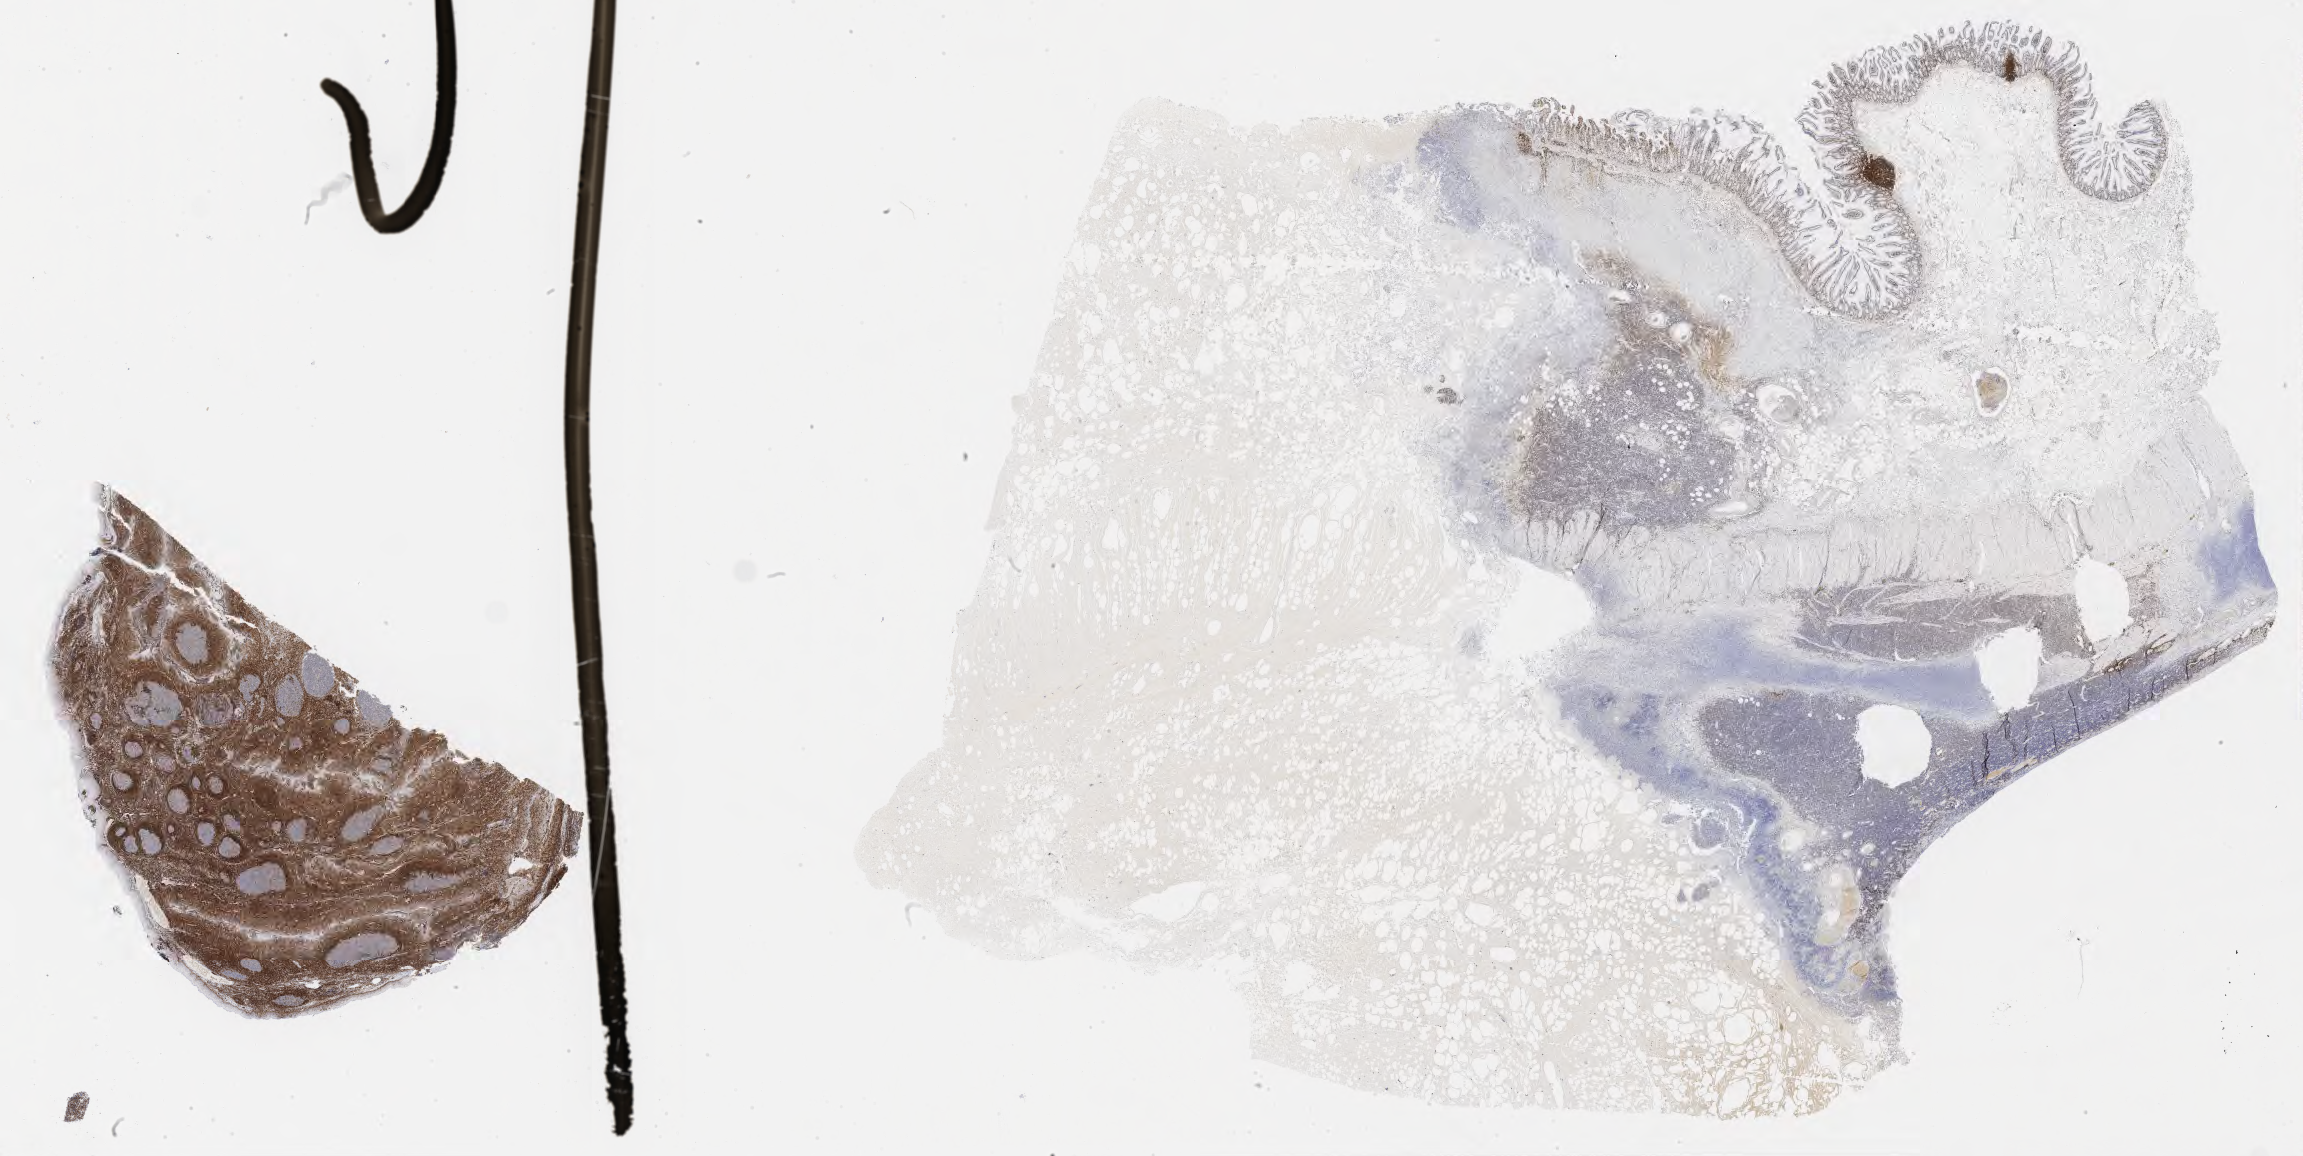
Whole-slide image, immunohistochemical stain for BCL2, a low-resolution overview of the entire scanned area, about 37.2 x 18.7 mm, tumor tissue, site: colon. Patient male; 62 years old.
Histologic diagnosis: Burkitt lymphoma, NOS.